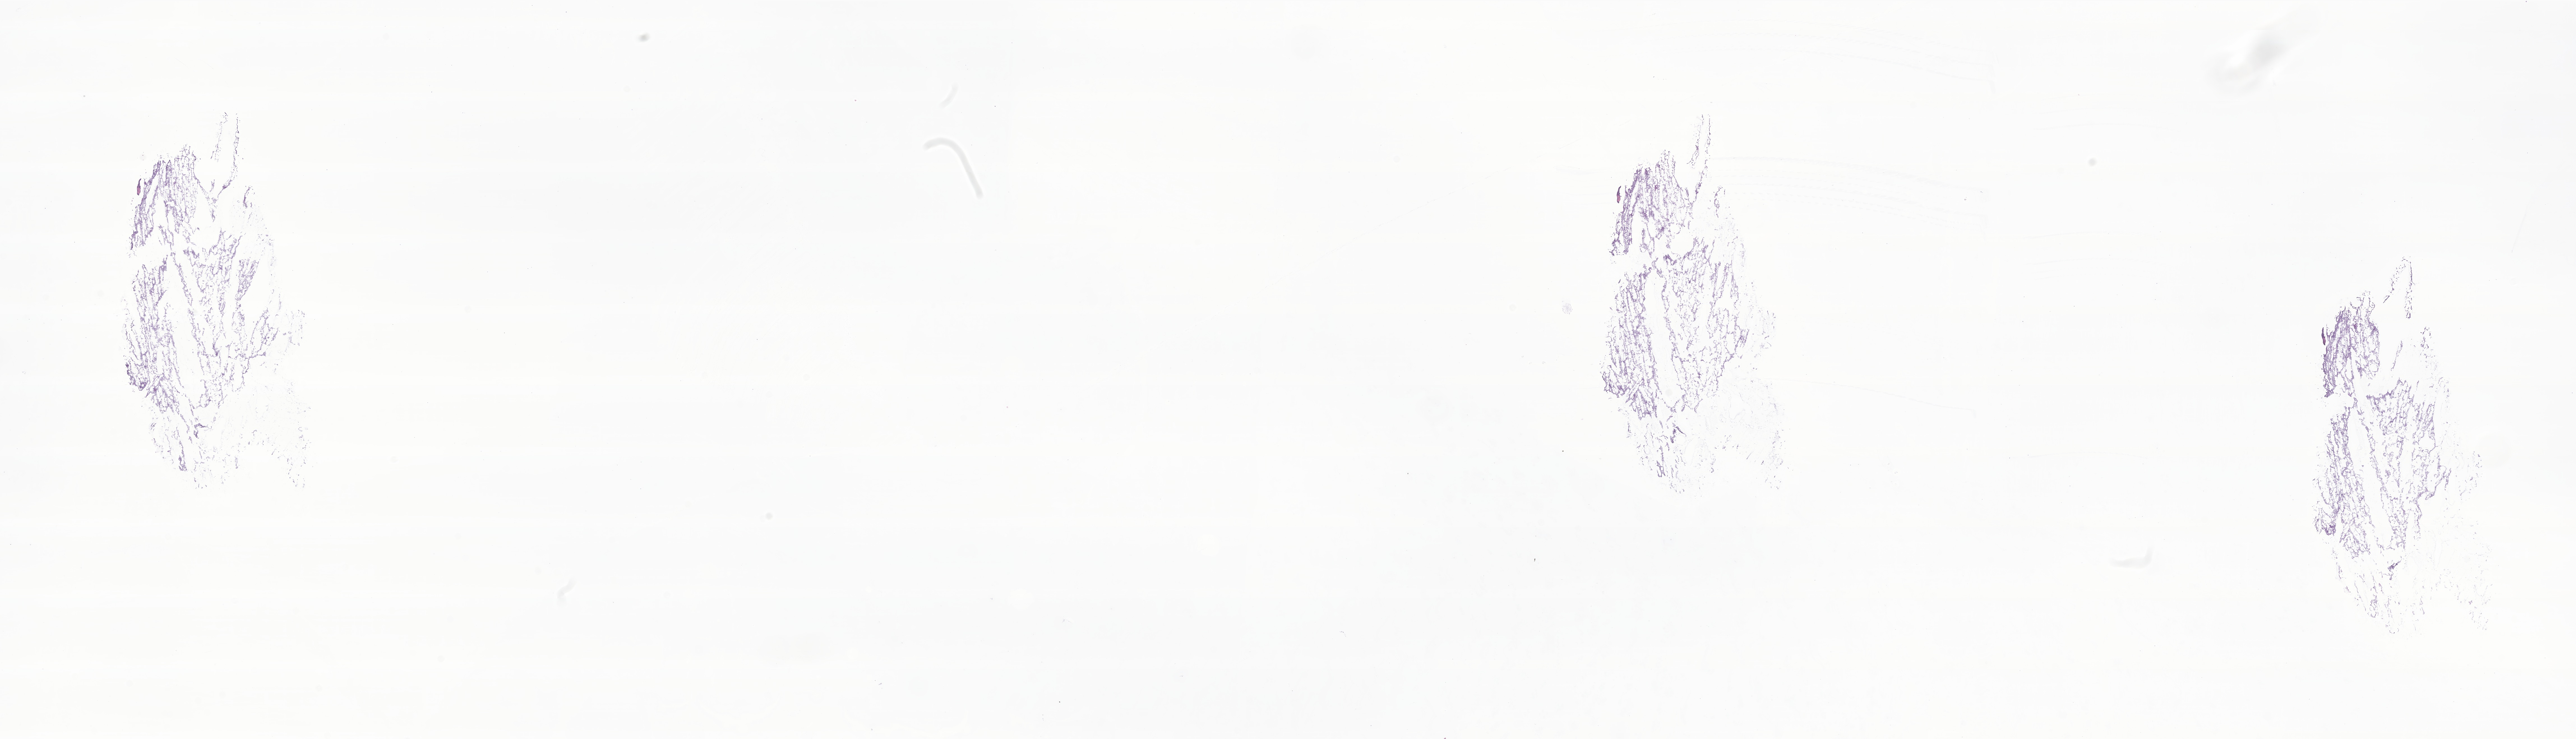
Hematoxylin and eosin (H&E) whole-slide image of tumor tissue from the testis — shown as a low-resolution overview of the whole scanned area (about 38.7 x 11.1 mm), cryosection (OCT / tissue freezing medium). Patient male; age 153 months (12 years 9 months).
Recorded diagnosis: Embryonal rhabdomyosarcoma, NOS.